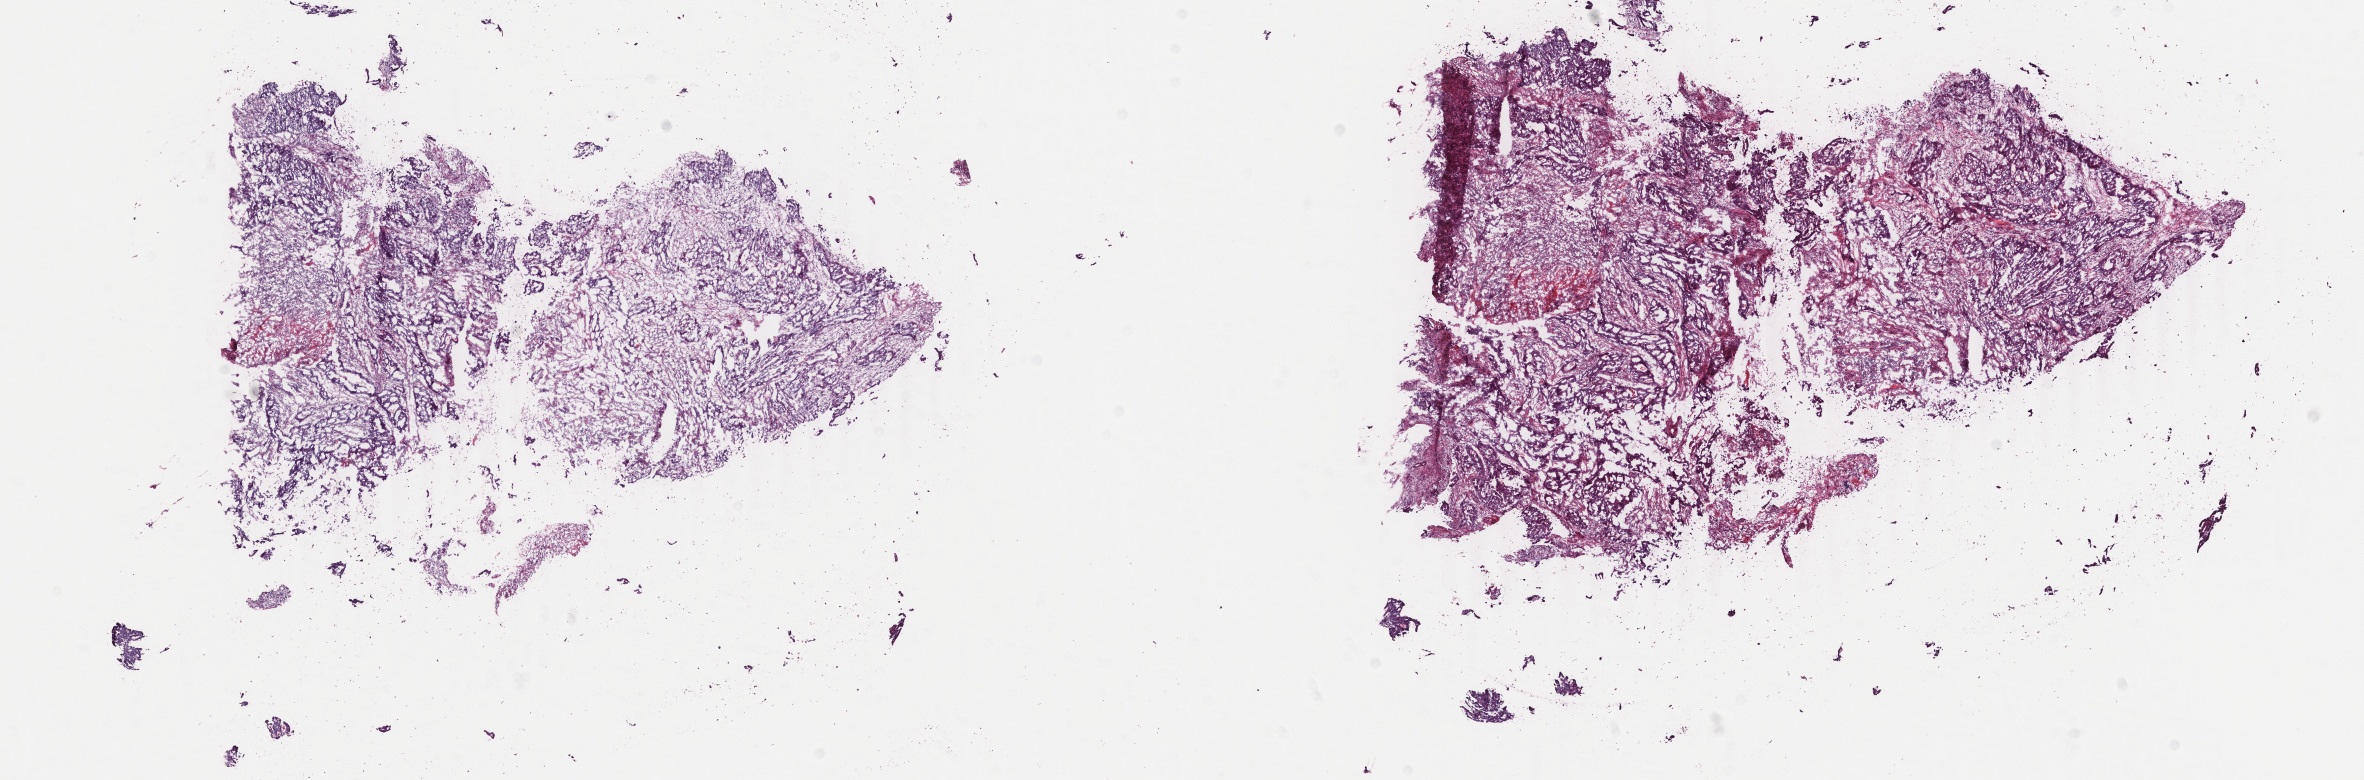
Whole-slide histology image, H&E, a low-resolution overview of the entire scanned area, about 18.8 x 6.2 mm (acquisition: 40x scan); frozen section from the bottom of the tissue portion; primary tumour sample from the colon. Female, age 68 years at initial diagnosis.
Pathologic diagnosis: Adenocarcinoma, NOS (sigmoid colon).